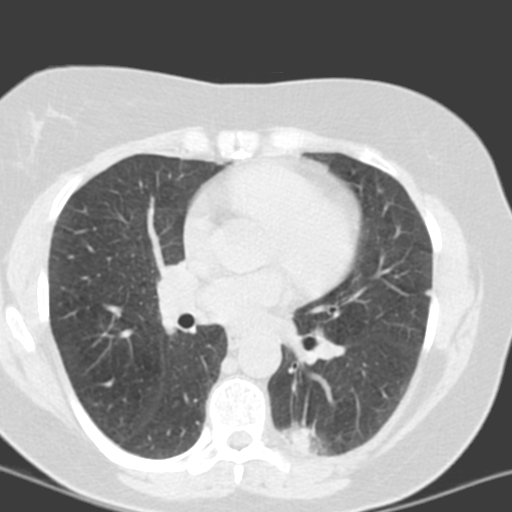
Chest CT (low-dose screening protocol), one axial image, third screening round (two years after baseline), lung window (W 1500 / L -600 HU), 3.2 mm slice thickness, 120 kVp. Female, age 55 years at enrolment. Current smoker at enrolment.
Expert-annotated lung lesion, bounding box (x1, y1, x2, y2) in pixels: (281, 407, 361, 462). The screening reader recorded 6 non-calcified nodules or masses ≥4 mm on this exam (left lower lobe, left lower lobe, left upper lobe, lingula, lingula, right middle lobe); which of them this box marks is not recorded. Participant outcome: lung cancer diagnosed 357 days after this screen — adenocarcinoma with mixed subtypes, left lower lobe, poorly differentiated (G3), stage IA (AJCC 6th edition), 21 mm at pathology.